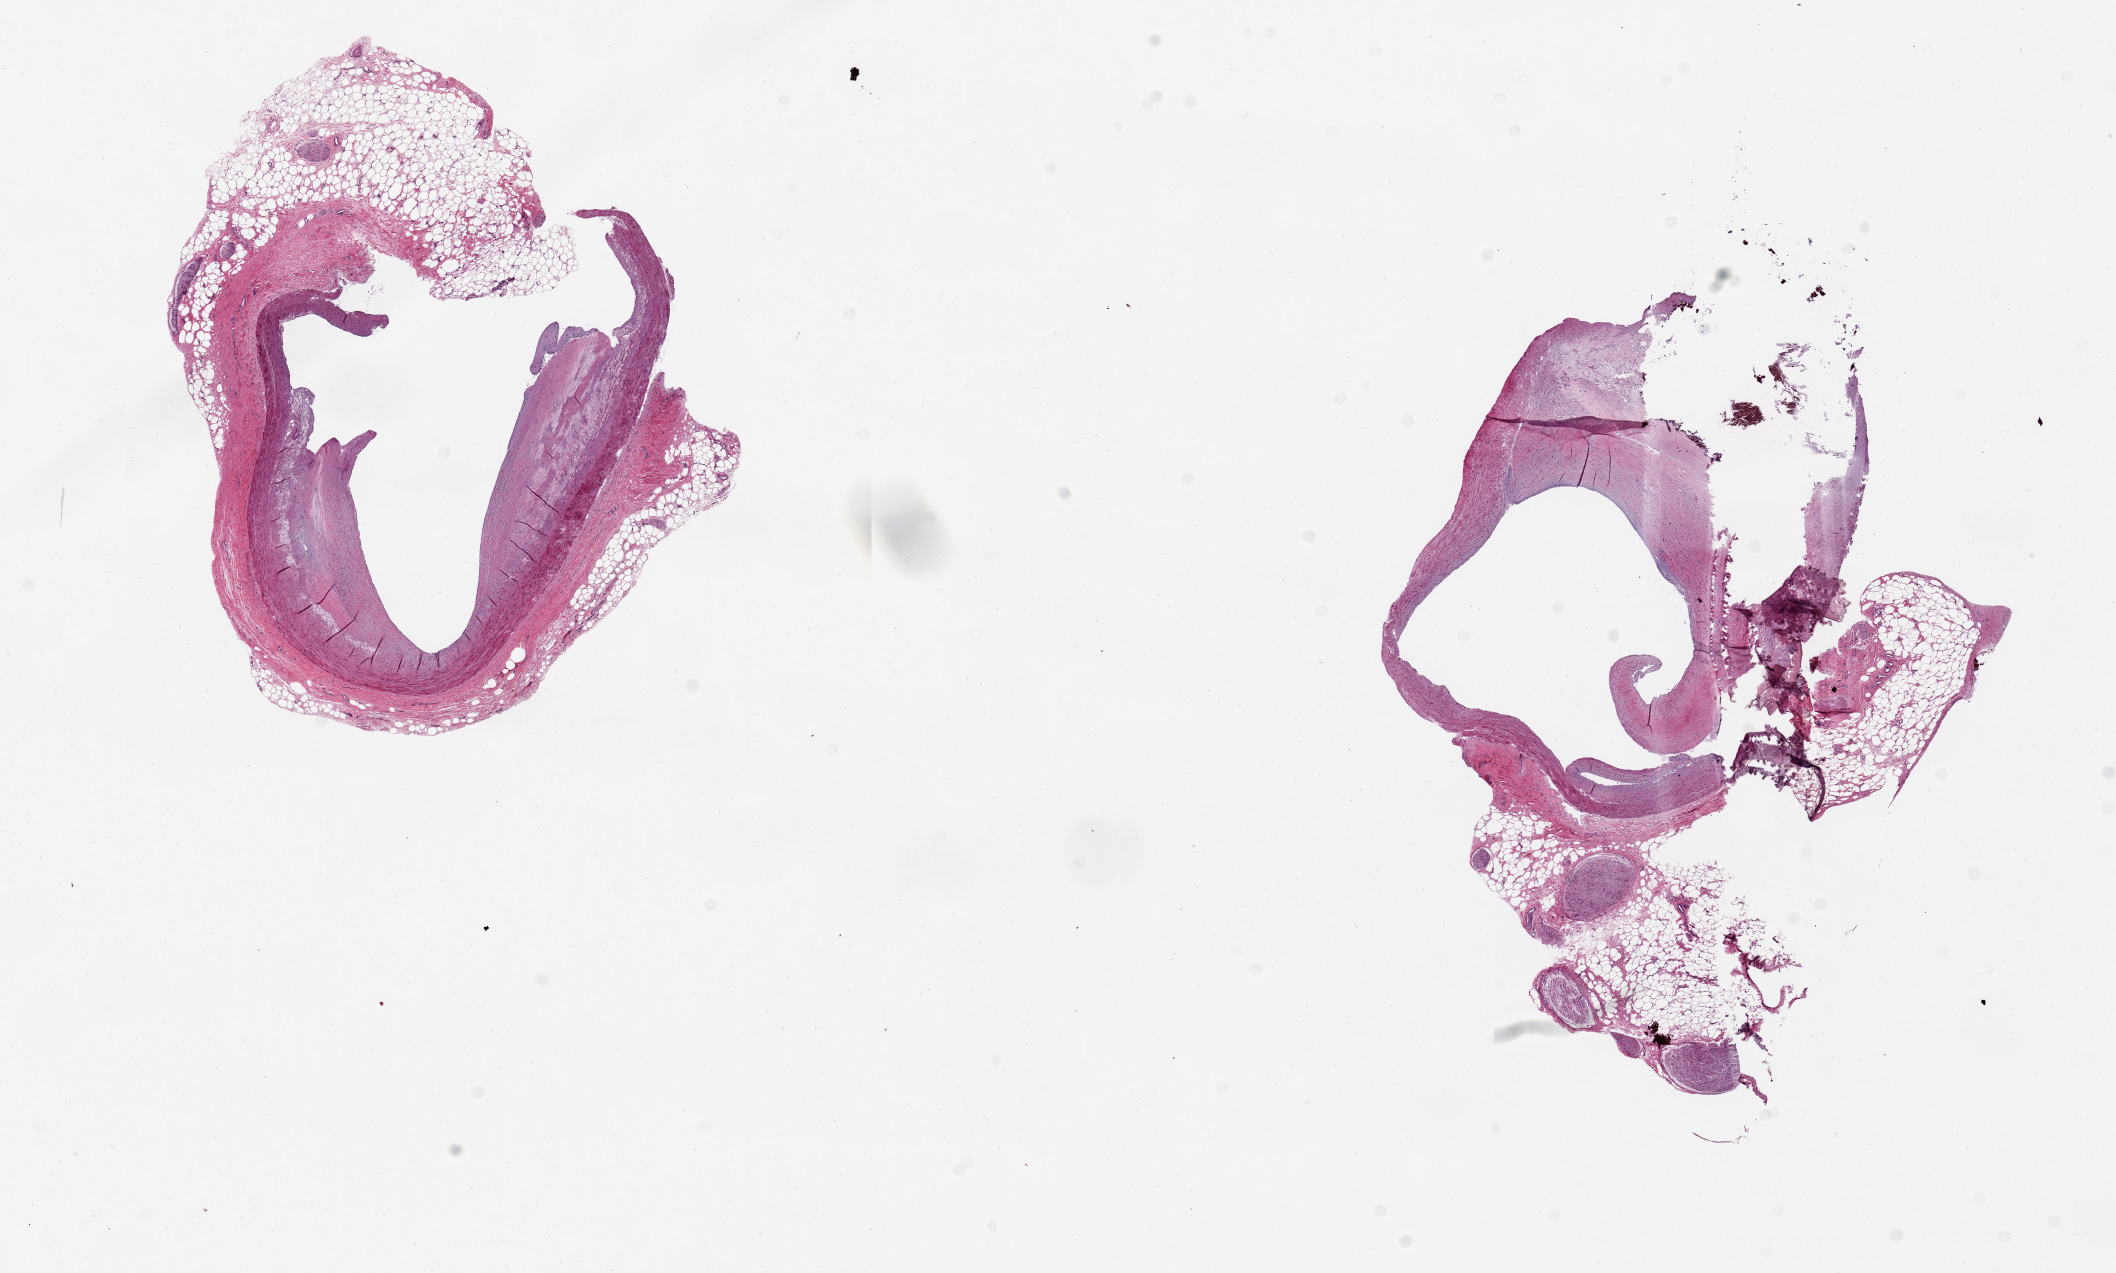
Whole-slide image, haematoxylin and eosin stain — shown as a low-resolution overview of the whole scanned area (about 16.7 x 10.1 mm, from a 20x scan); PAXgene-fixed, paraffin-embedded tissue; target tissue: coronary artery; tissue donor sample. Donor sex: female.
Pathologist's review note for this sample: 2 pieces, 6x4.5 & 7x5mm; nubbins of adherent fat on both, up to ~2.5mm; 40-50% occlusive atherosclerosis, focally calcified.